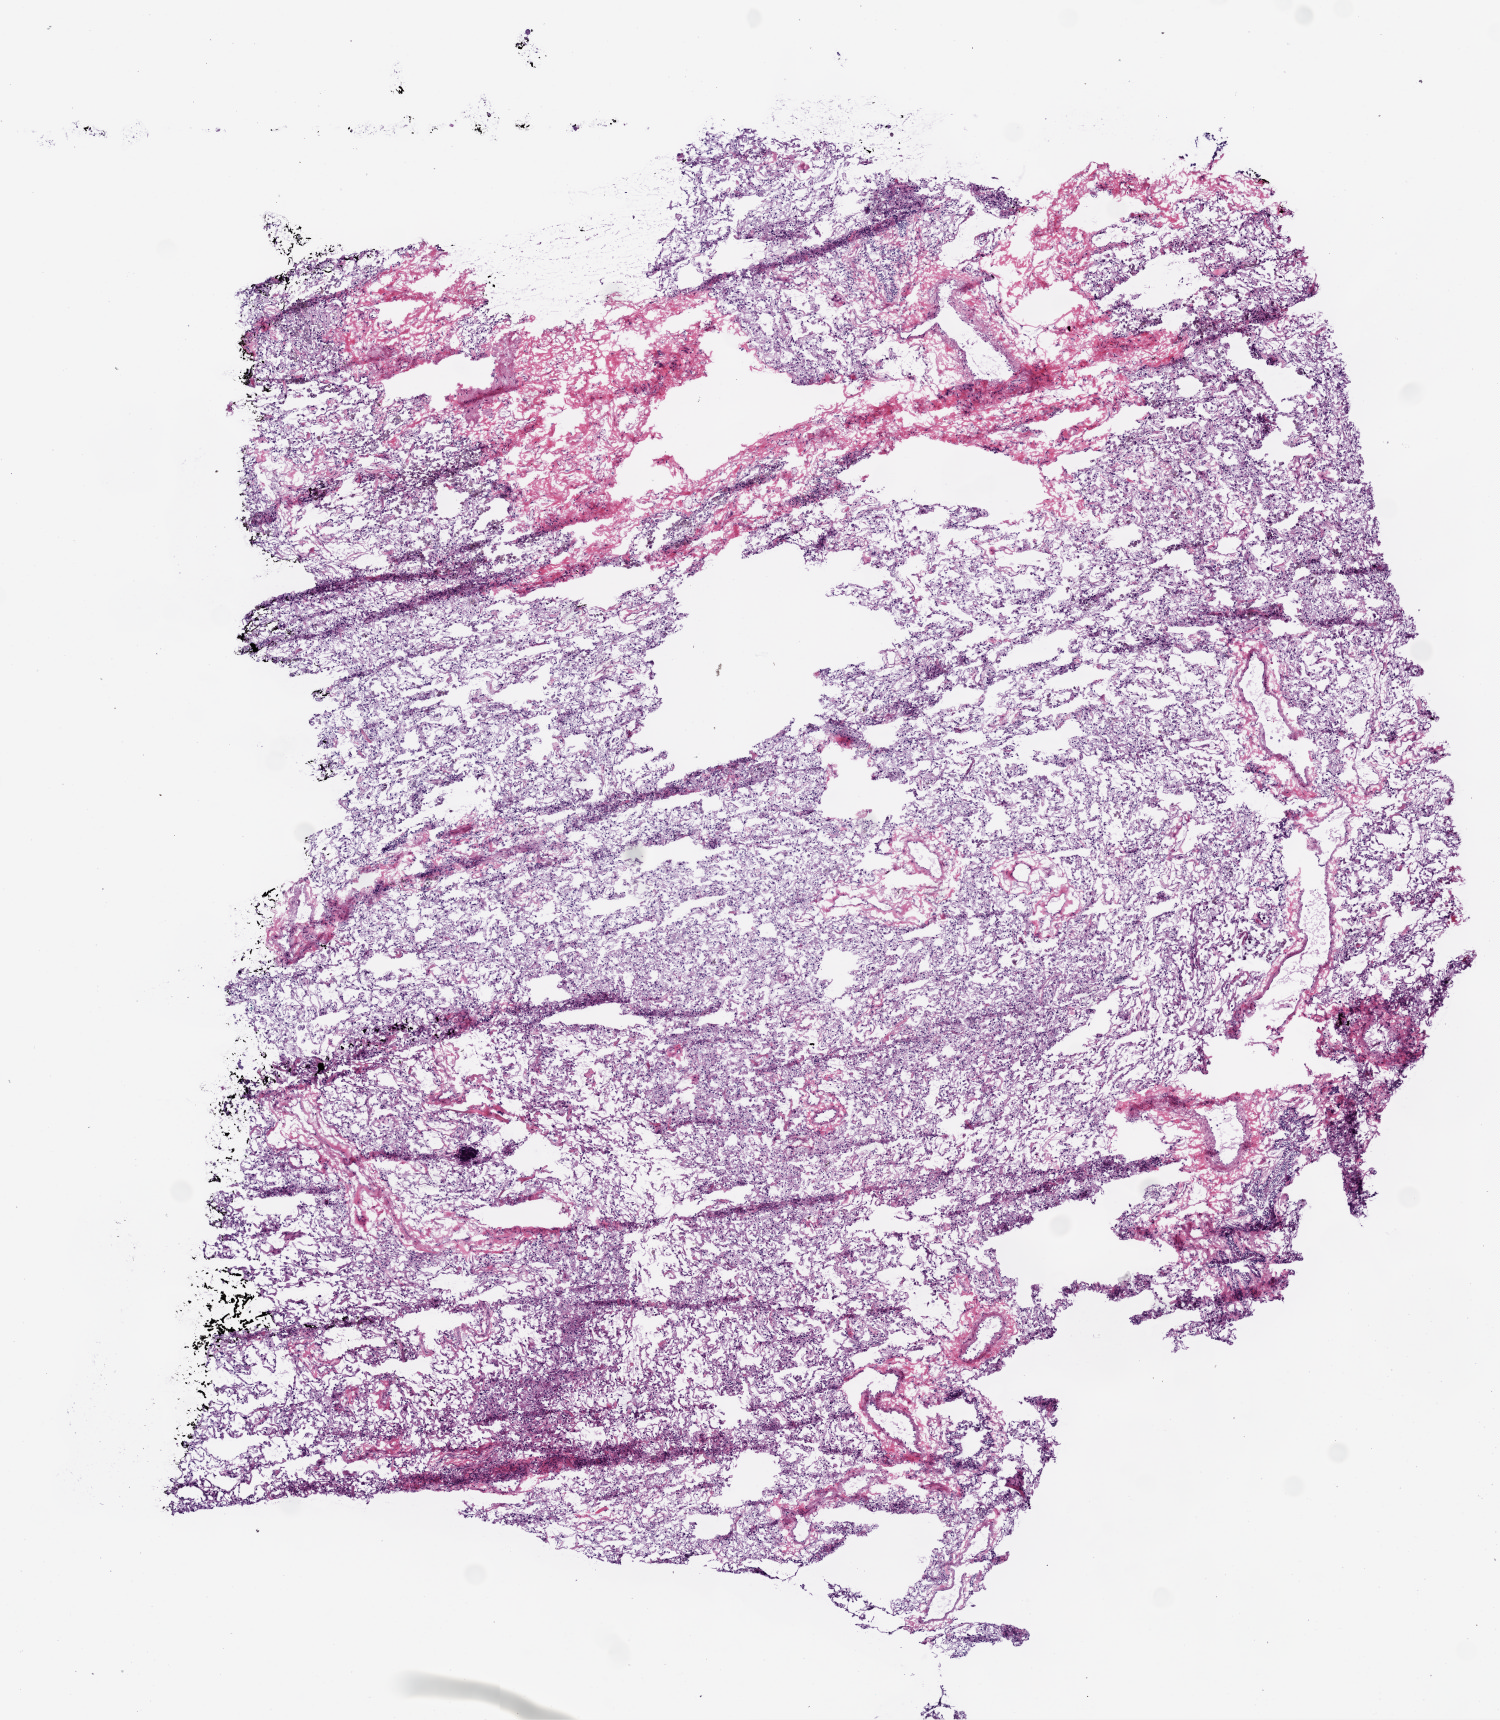
H&E whole-slide image, a low-resolution overview of the entire scanned area, about 6.0 x 6.9 mm (slide scanned at 20x). Frozen section from the top of the tissue portion. Solid tissue normal (non-tumour tissue) sample from the lung. Male, age 68 years at initial diagnosis.
- this section: solid tissue normal sample (biorepository sample class)
- patient diagnosis: Adenocarcinoma, NOS (lower lobe, lung)